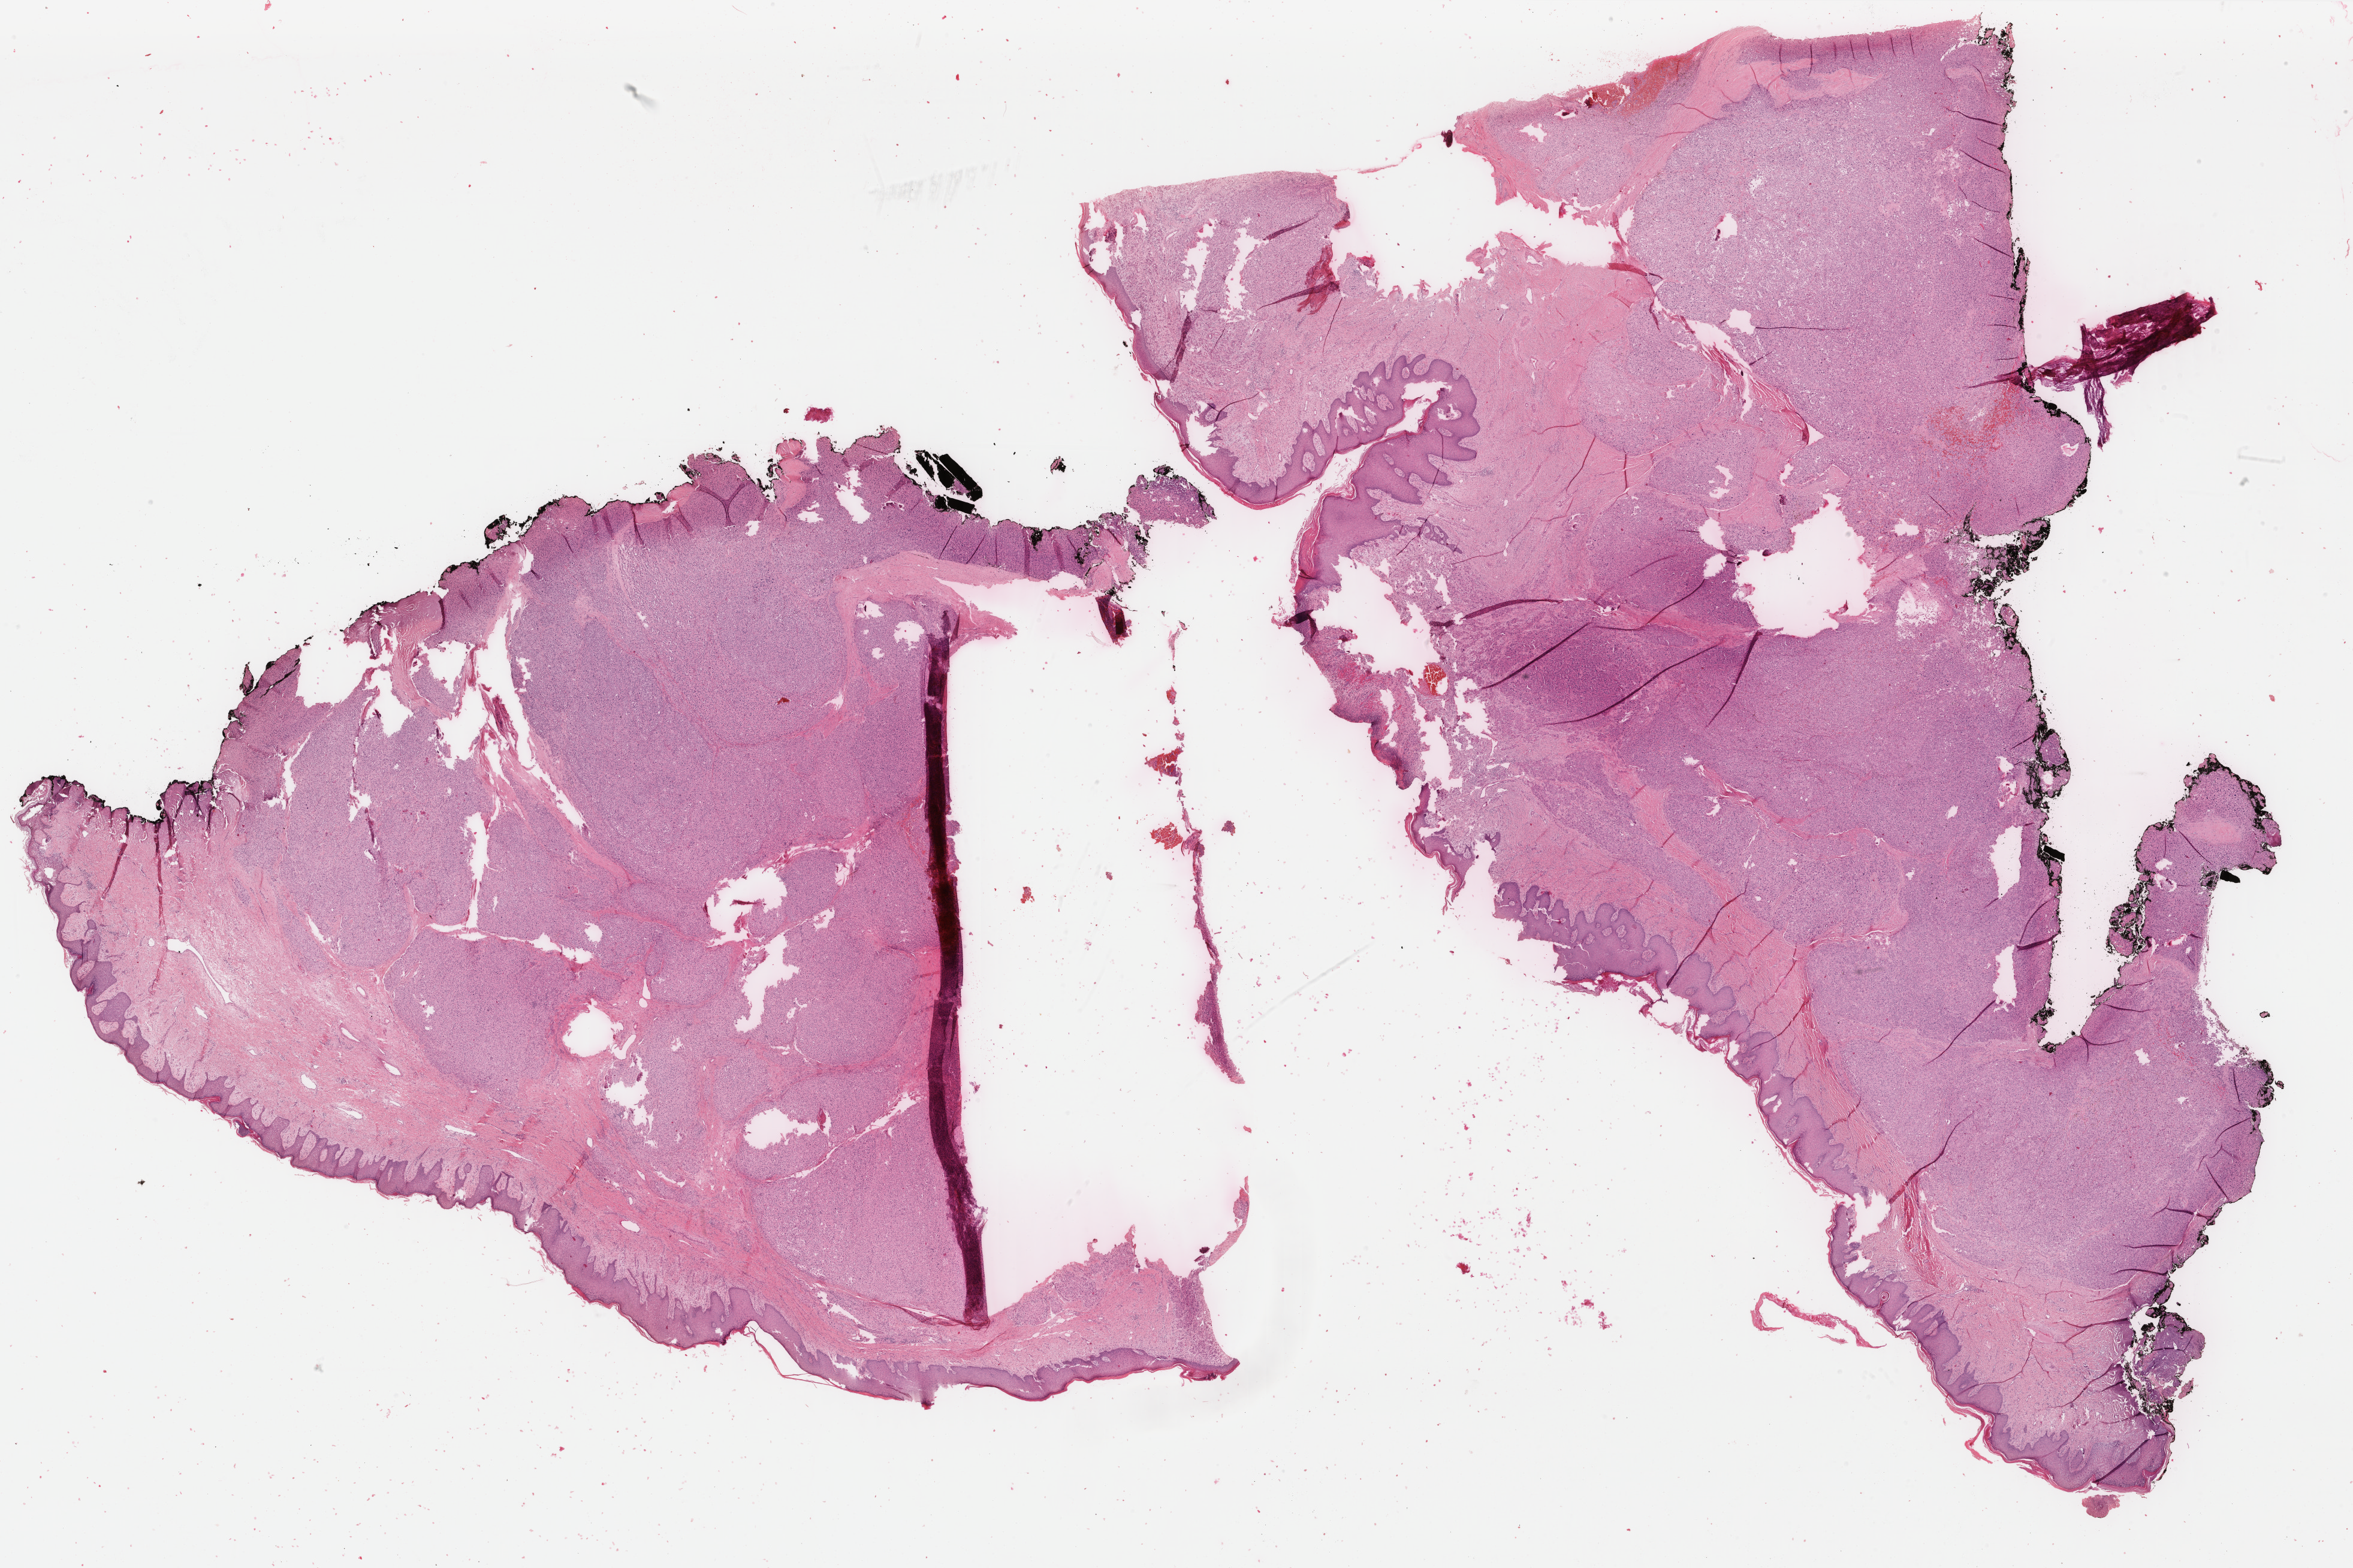
Digitized H&E-stained tissue section (whole slide), whole scanned area (about 31.2 x 20.8 mm) shown as a low-resolution overview, formalin-fixed paraffin-embedded (FFPE) diagnostic section, sample: primary tumour, skin. Female, age 58 years at initial diagnosis.
Pathologic diagnosis: Malignant melanoma, NOS.